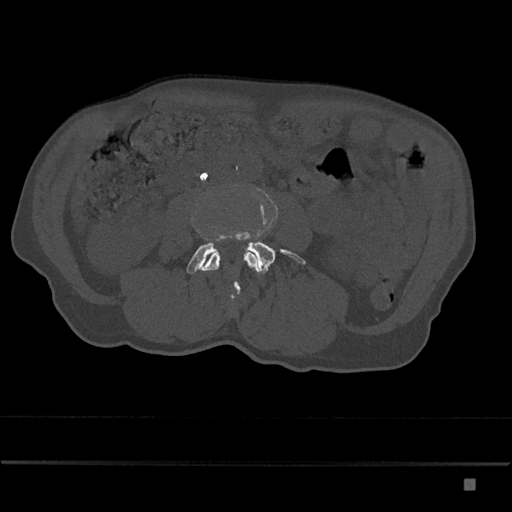
CT including the spine, one axial slice; reconstruction kernel Br40s/3; 120 kVp; bone window (W 1800 / L 400 HU); 0.5 mm slice thickness; 512 × 512 image matrix. Patient: male, 72 years. Case-level facts recorded for this patient, not image findings: primary cancer: prostate.
Structures marked on this image (semi-automatically segmented with operator editing):
- L3 vertebra: box from (x=202, y=252) to (x=259, y=294) px
- L4 vertebra: (x=186, y=230)–(x=306, y=301)